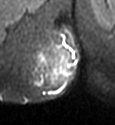
MRI of an extremity soft-tissue mass, one axial slice; slice 13 of 49 in the series (ordered by position); STIR; MR volume resampled by the dataset authors to the PET/CT grid (not the native acquisition matrix); 3.27 mm slice thickness; 115 × 125 image matrix, field of view 112 × 122 mm. Female patient. Case-level facts recorded for this patient, not image findings: histological type: epithelioid sarcoma; grade: intermediate; site of the primary tumour: right buttock.
Structures marked on this image (expert contour drawn on MRI and transferred to this co-registered scan by the dataset authors):
- gross tumour volume including surrounding oedema: bounding box [x1, y1, x2, y2] px = [31, 37, 78, 99]
- gross tumour volume (mass): [47, 48, 55, 60]